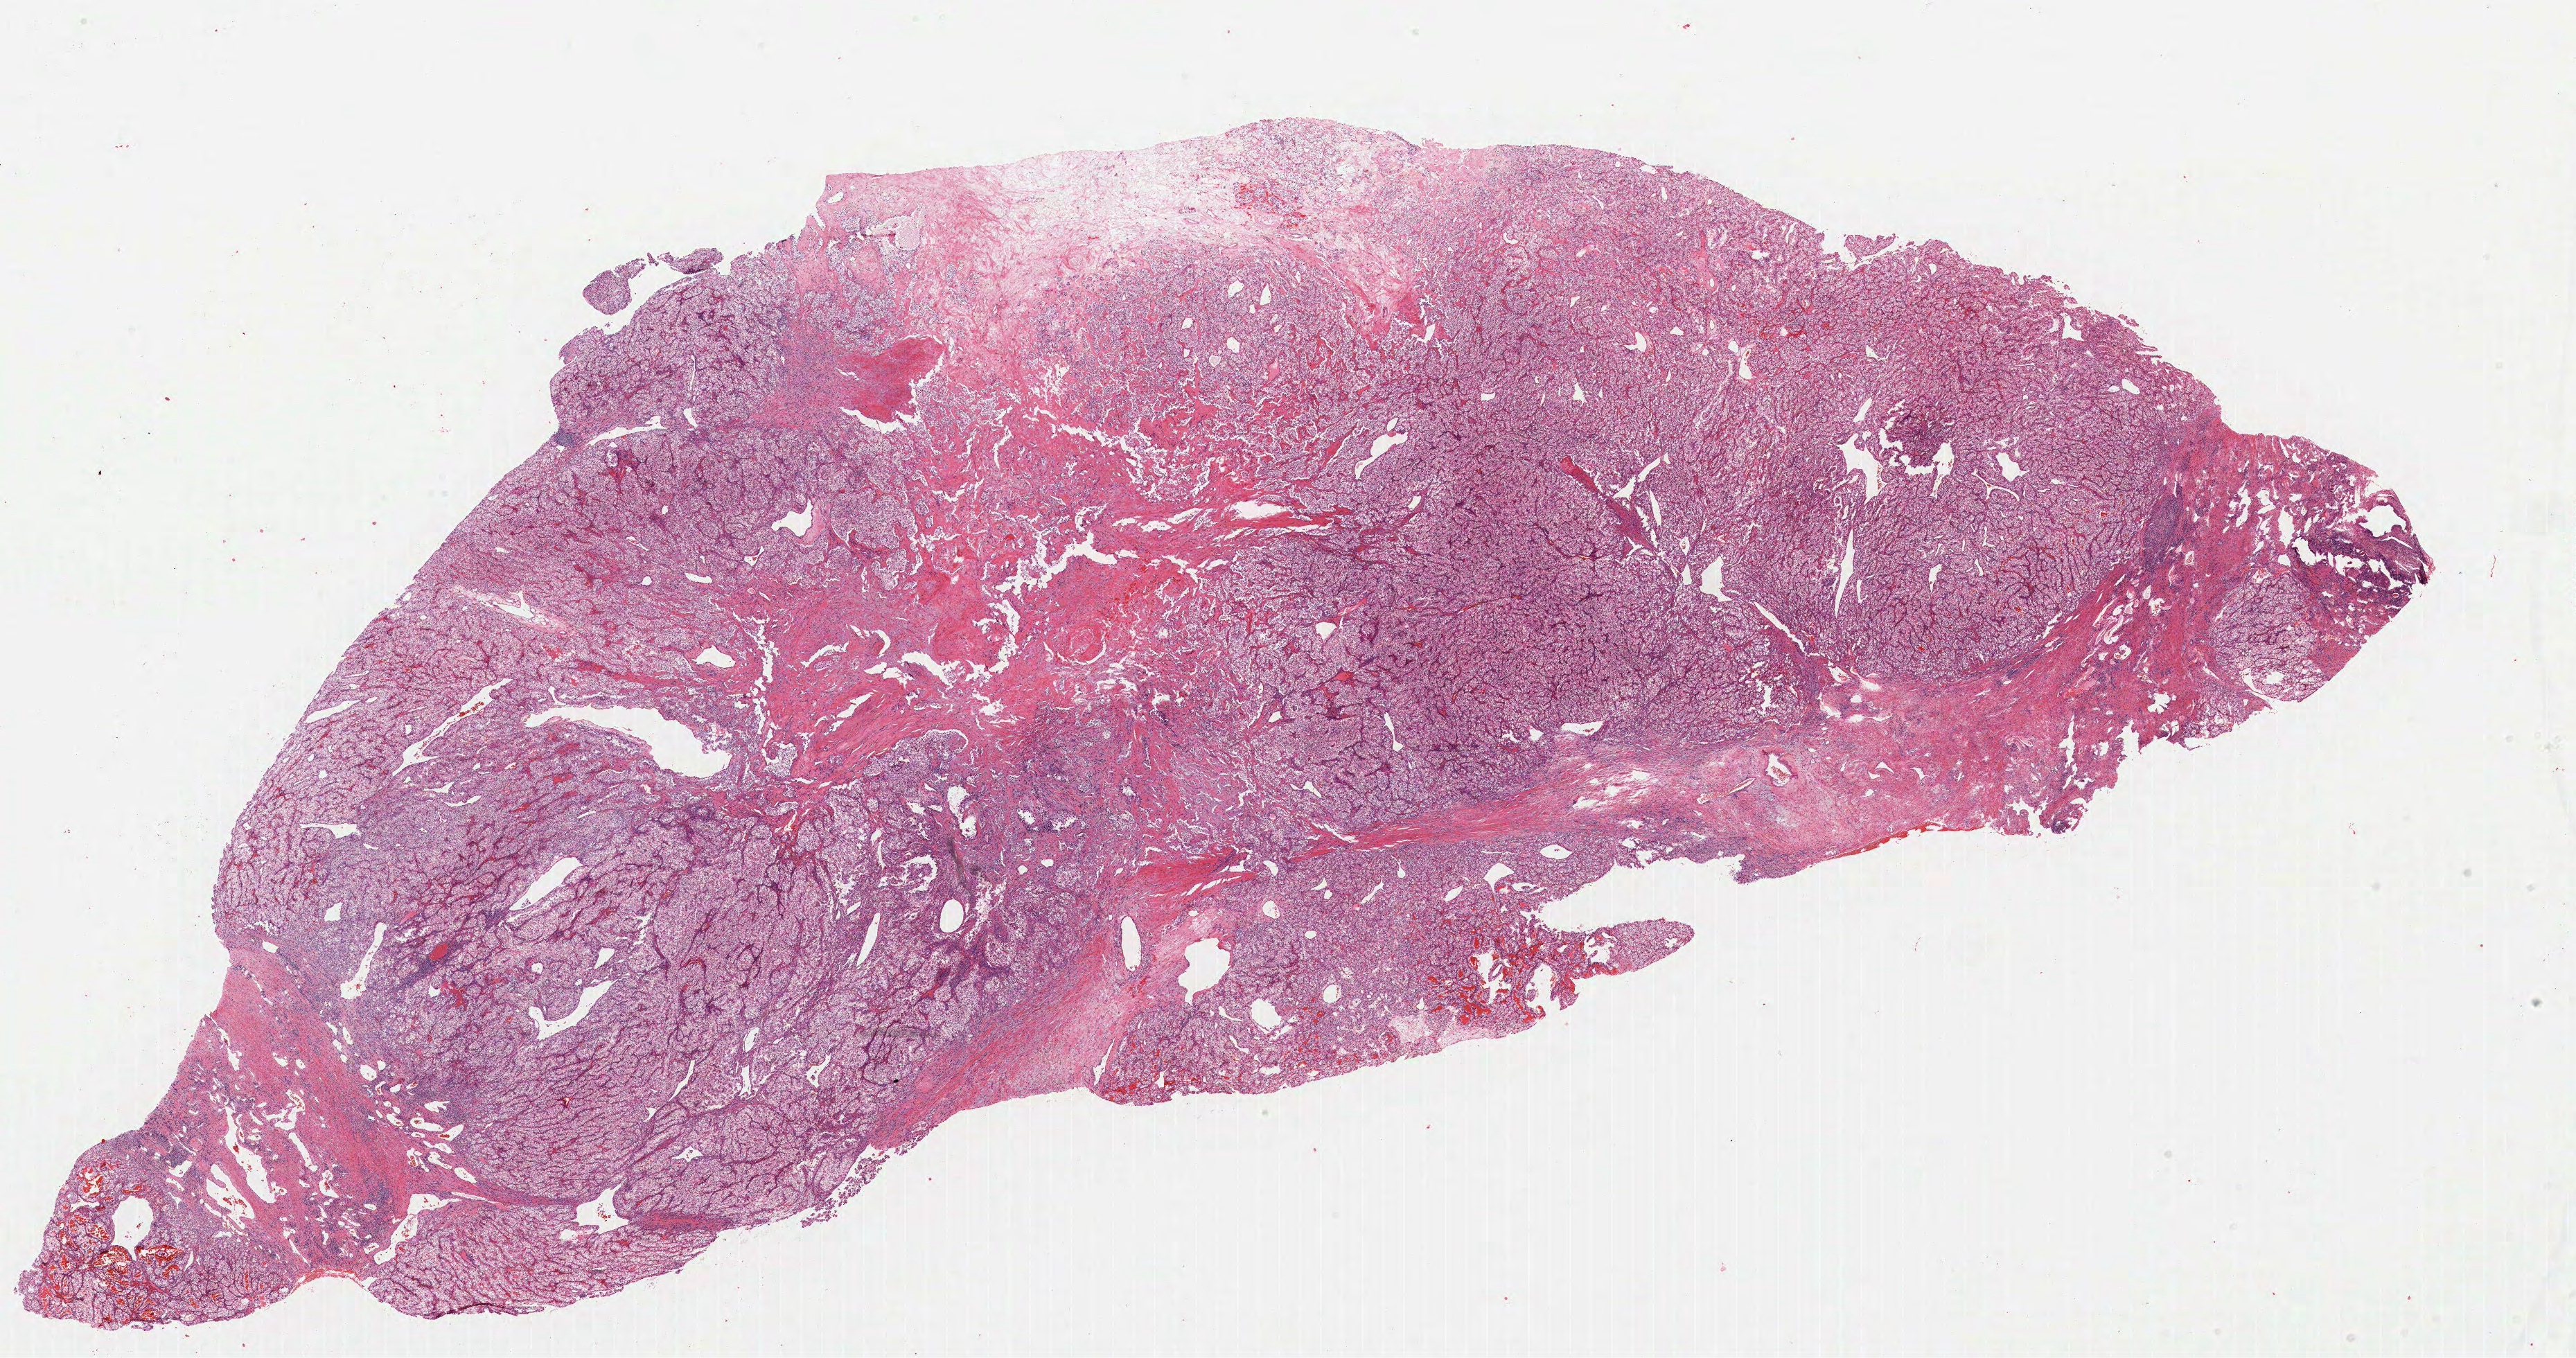
Digitized Hematoxylin and eosin (H&E) stained tissue section (whole slide), whole scanned area (about 30.0 x 15.8 mm) shown as a low-resolution overview, formalin-fixed paraffin-embedded (FFPE) diagnostic section, kidney, primary tumour sample. Male patient; age at initial diagnosis 51 years. Histologic grade: G3 (poorly differentiated).
Pathologic diagnosis: Clear cell adenocarcinoma, NOS. AJCC pathologic stage: I (6th edition). Laterality: left.